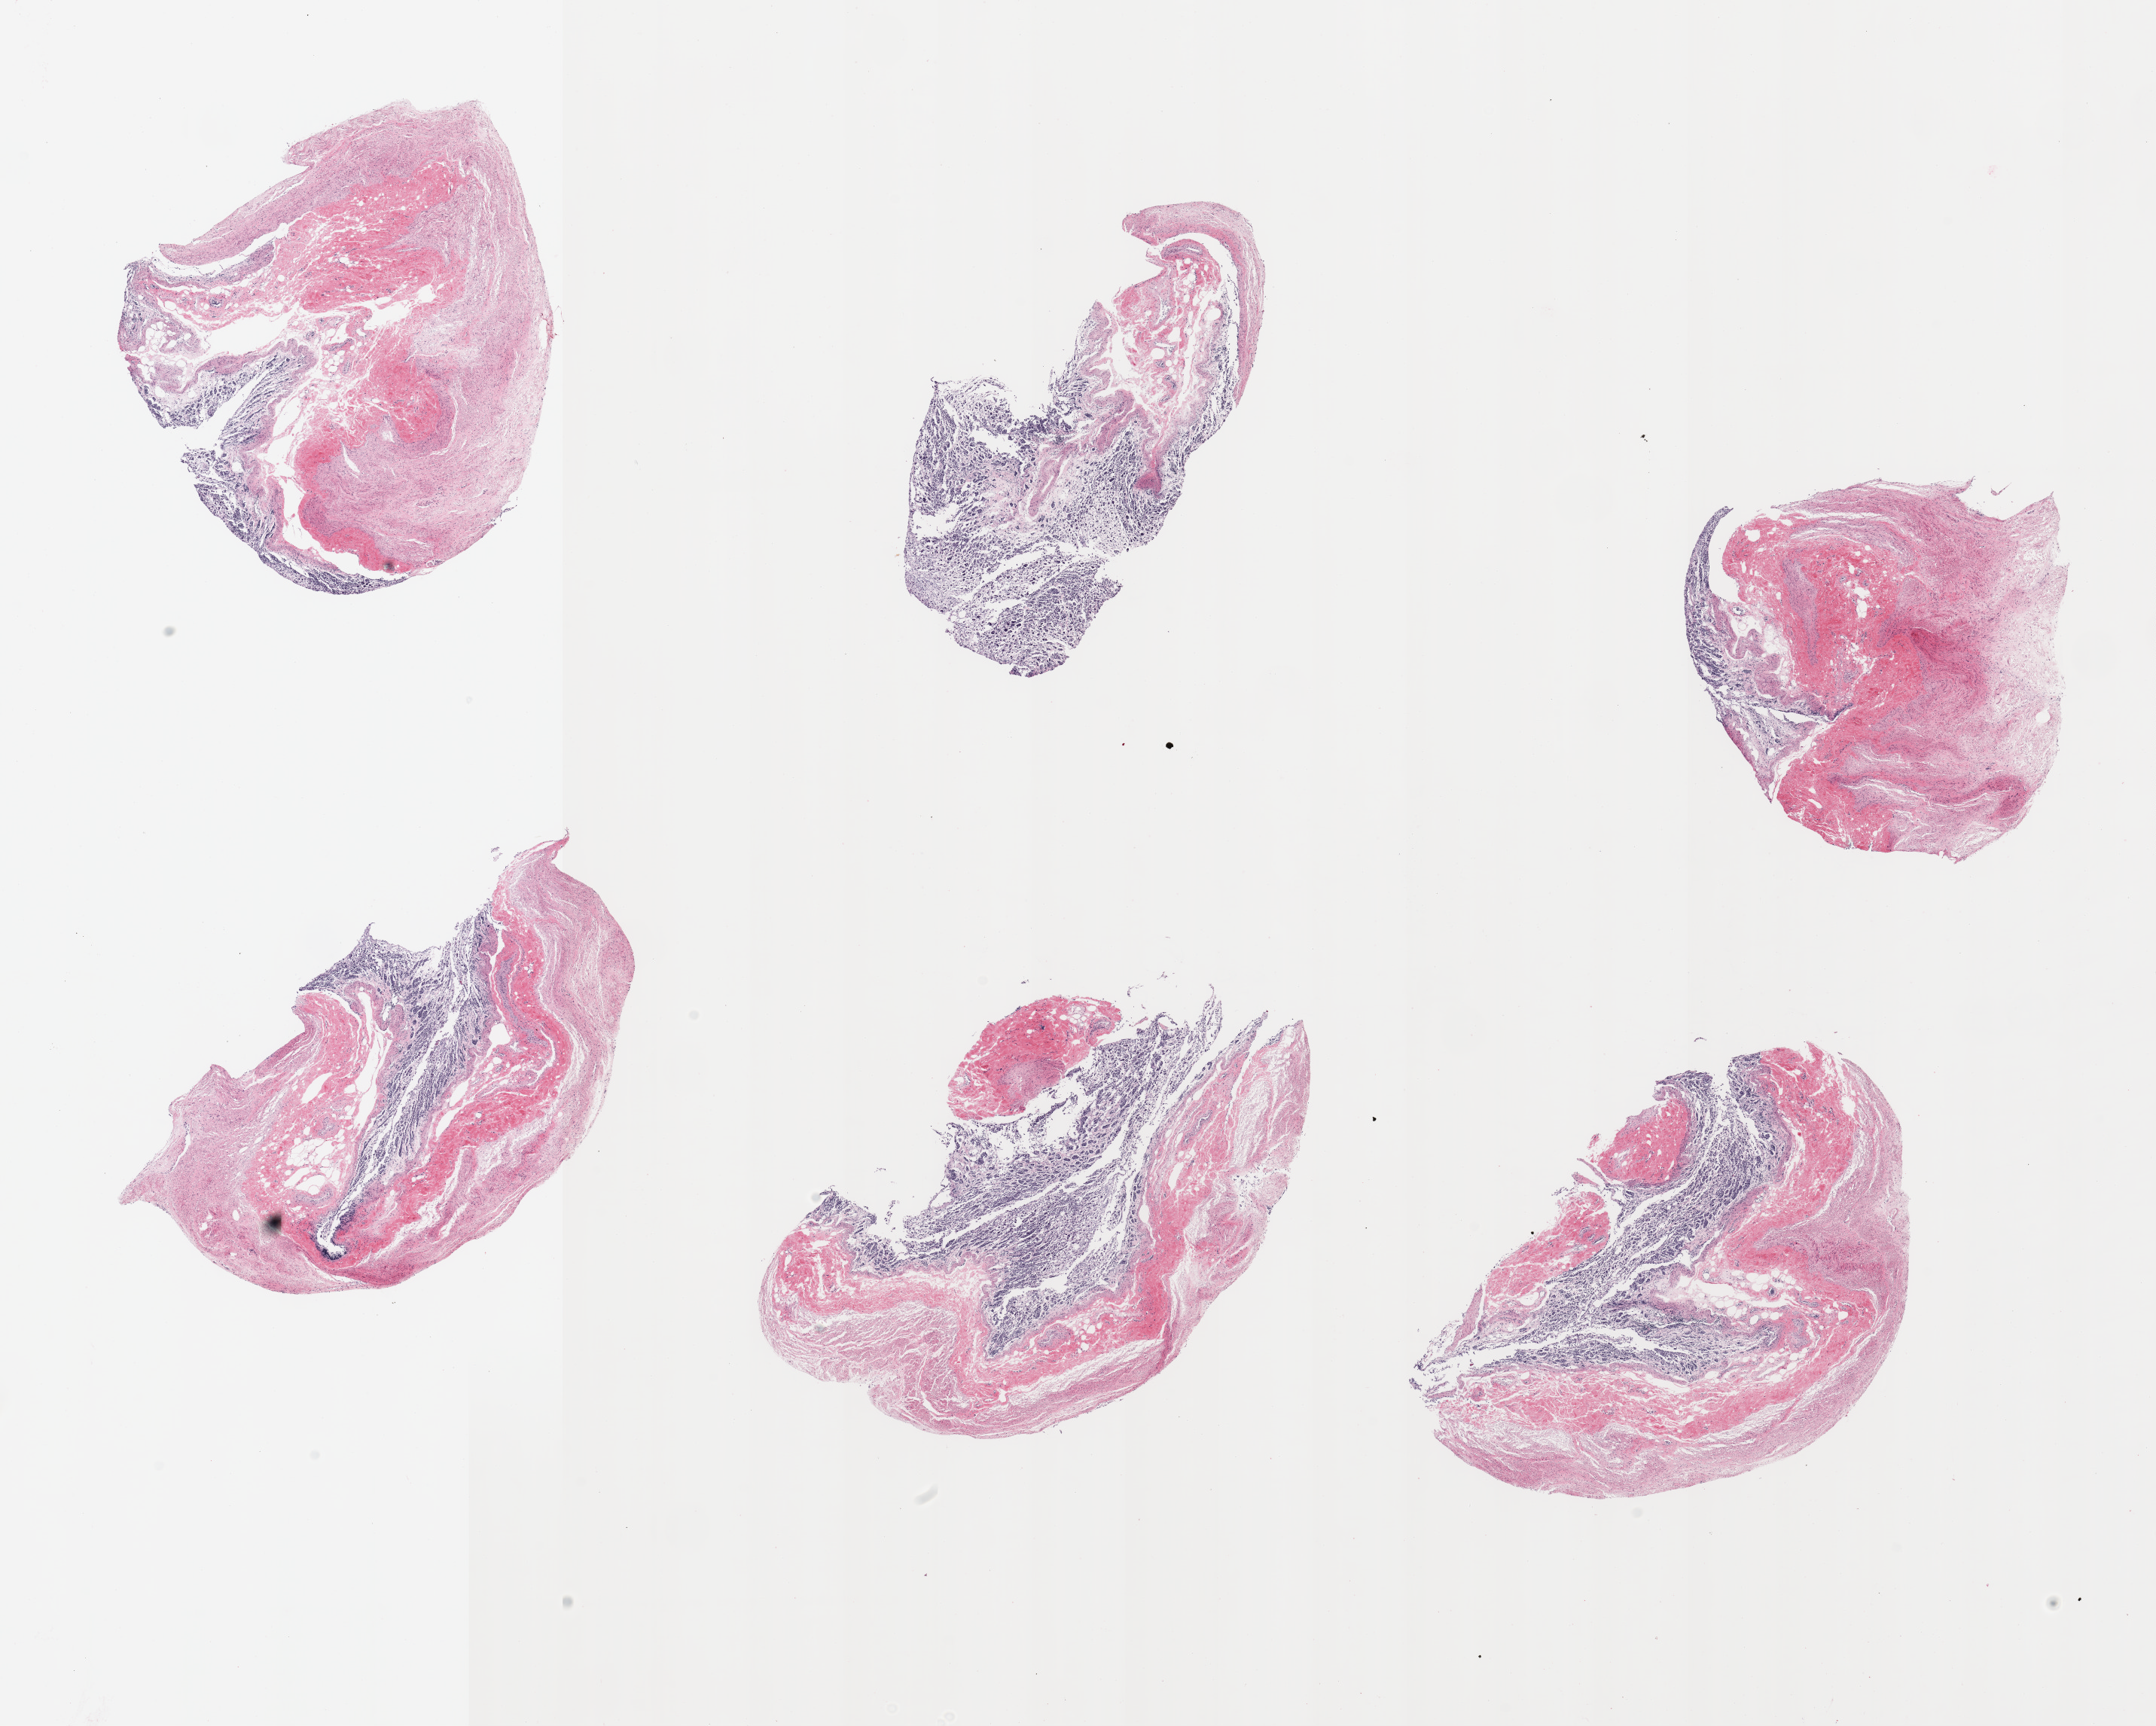
Whole-slide image, hematoxylin and eosin (H&E) stain, low-resolution overview of the scanned area, about 22.6 x 18.1 mm (slide scanned at 20x). PAXgene-fixed paraffin-embedded (PFPE) section. Sampled site (target tissue): stomach. Tissue donor sample. Donor sex: male.
Pathologist's review note for this sample: 6 pieces; severely autolyzed full thickness sections.